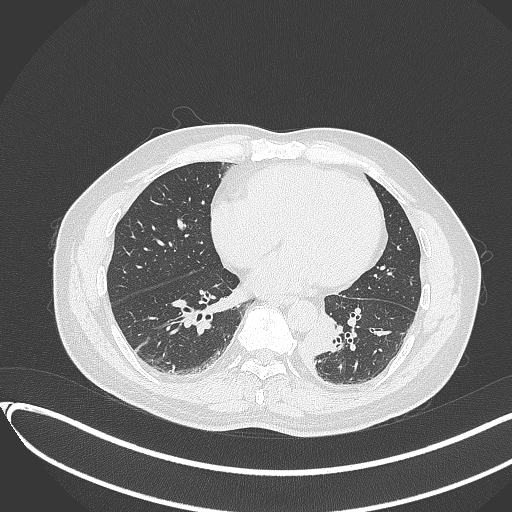
Chest CT, one axial slice. Reconstruction kernel B70f. 120 kVp. Lung window (W 1500 / L -600 HU). 512 × 512 image matrix, field of view 400 × 400 mm. Patient: male, 54 years. From the clinical record (not read from this slice): clinical TNM (as recorded): T3 N0 M0.
Annotated regions visible in this slice (rectangle marked by the reading radiologist):
- lung tumour (recorded histology: squamous cell carcinoma): bounding box (x1, y1, x2, y2) in pixels: (300, 308, 345, 368)